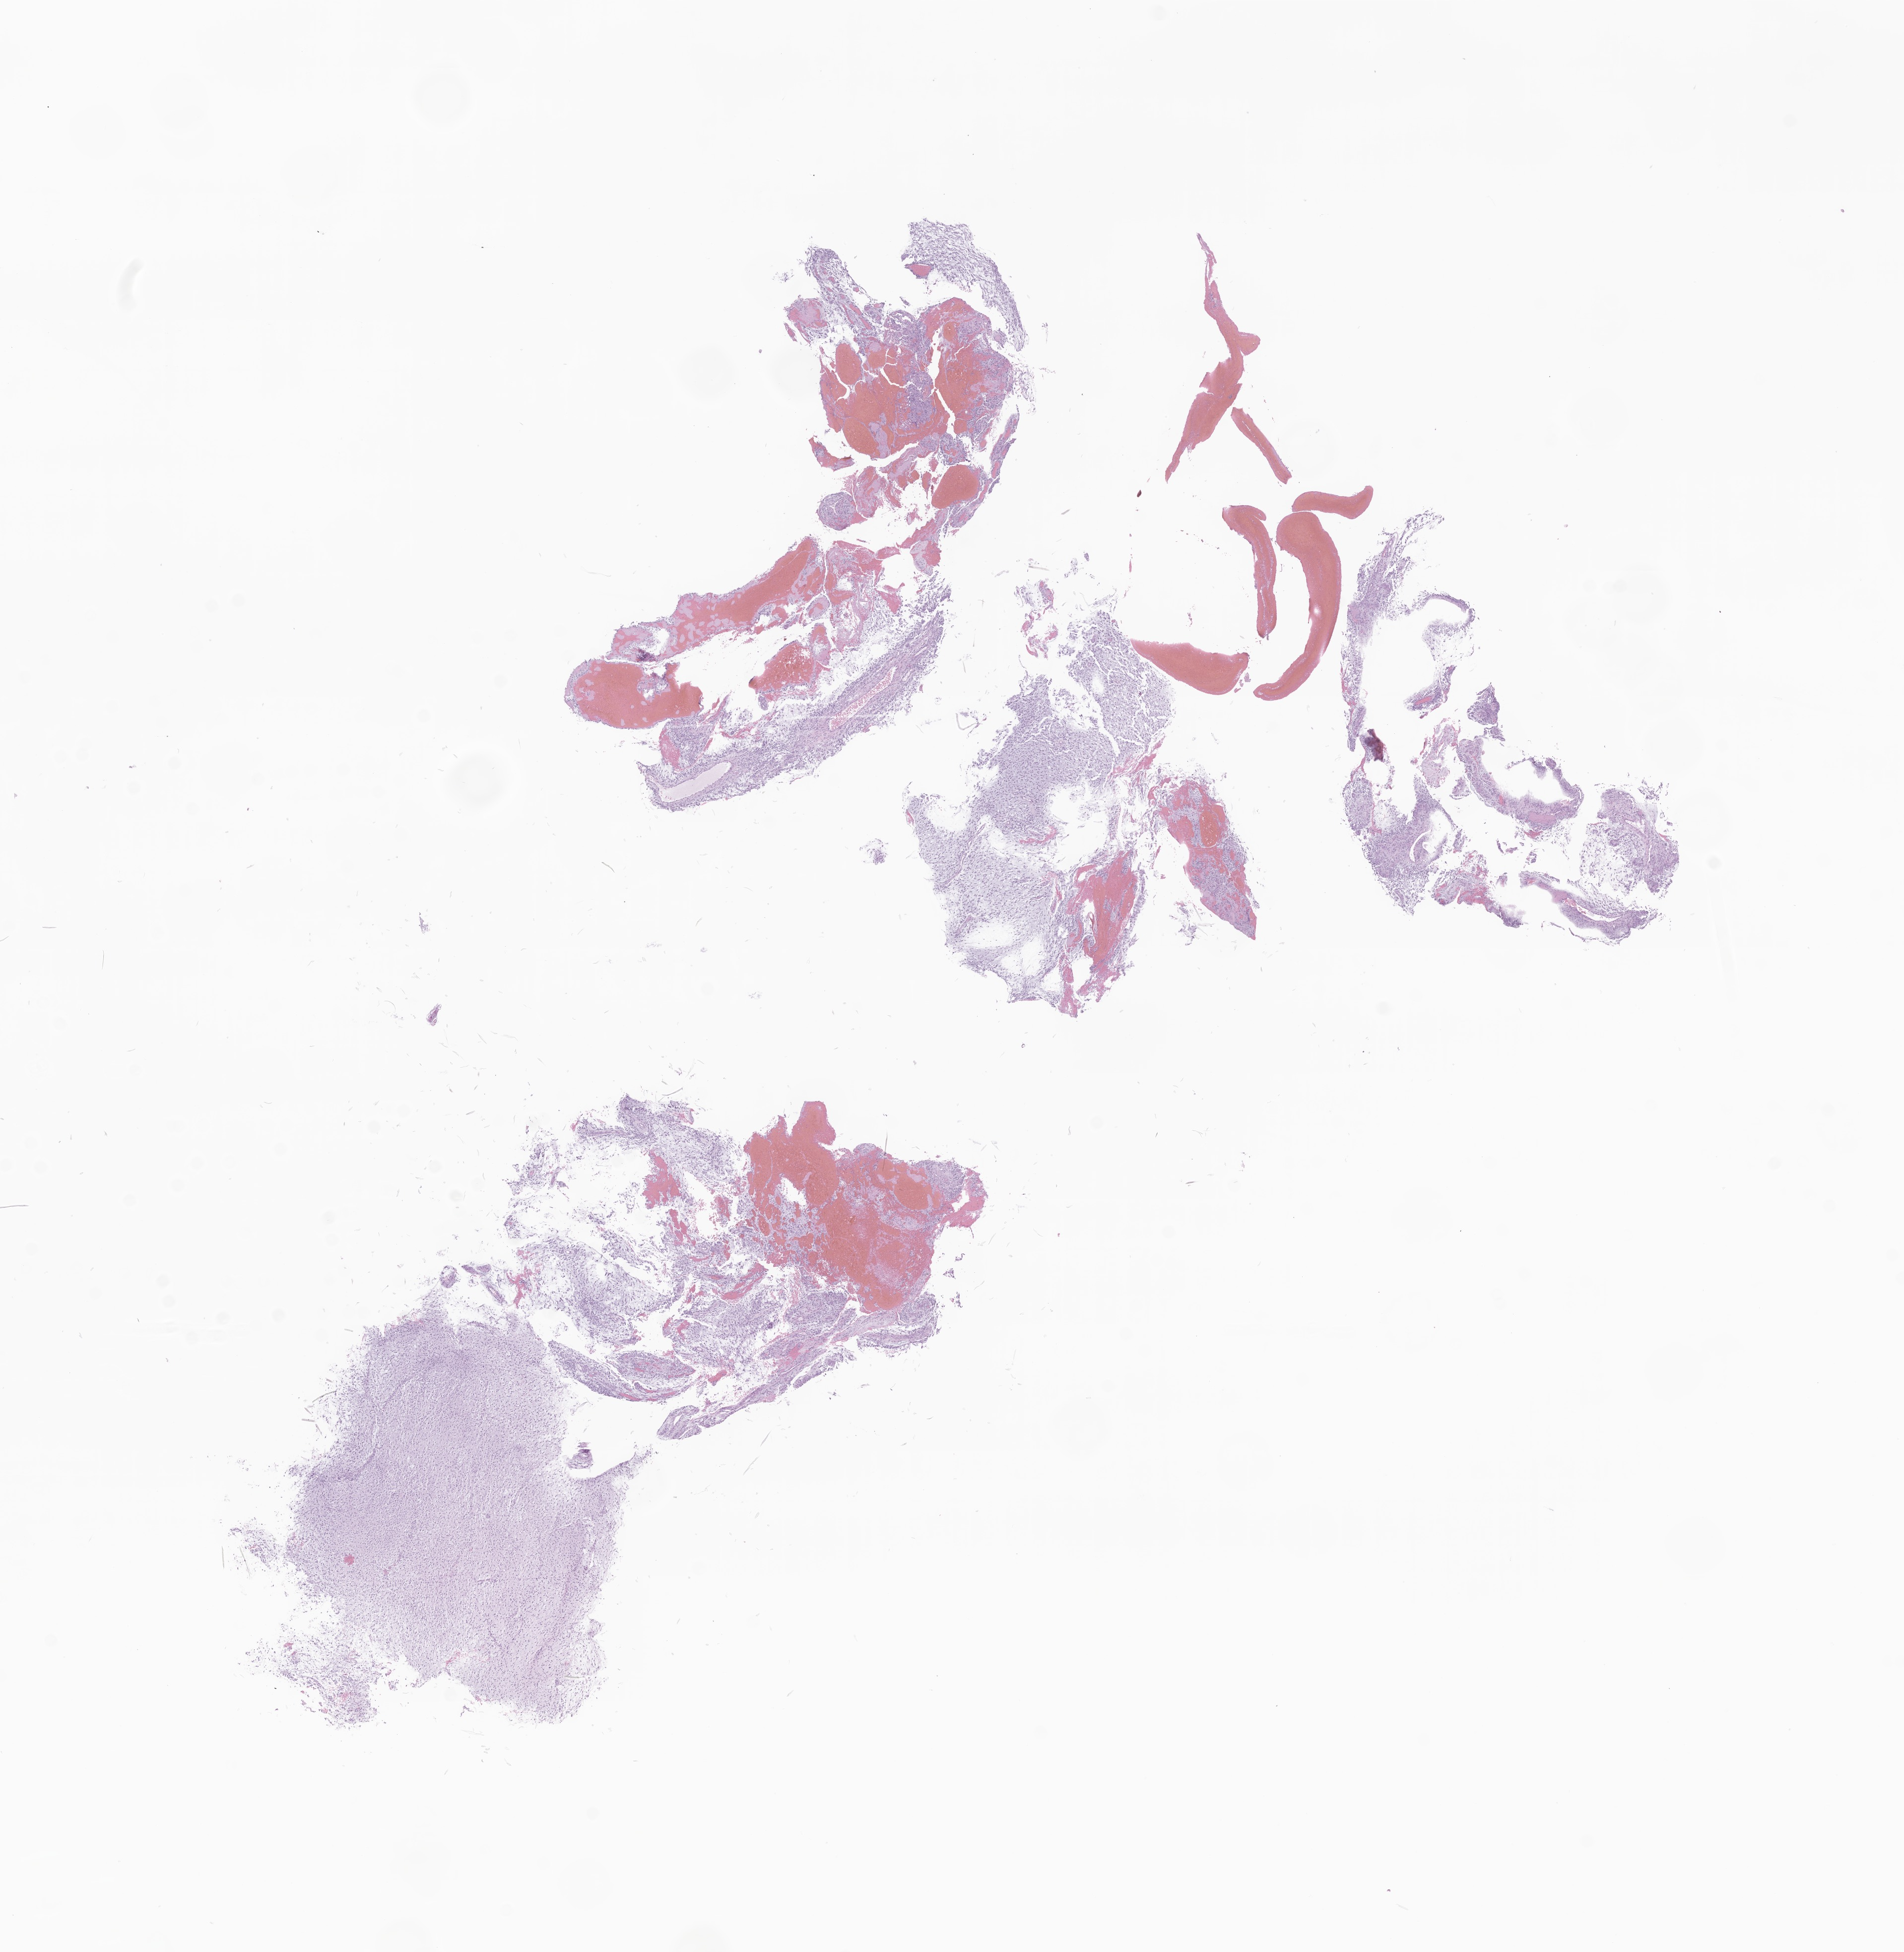
H&E whole-slide image of tumor tissue from the brain, whole scanned area (about 16.2 x 16.6 mm) shown as a low-resolution overview, FFPE section. Patient: male, age 323 days.
• diagnosis: Pilocytic astrocytoma